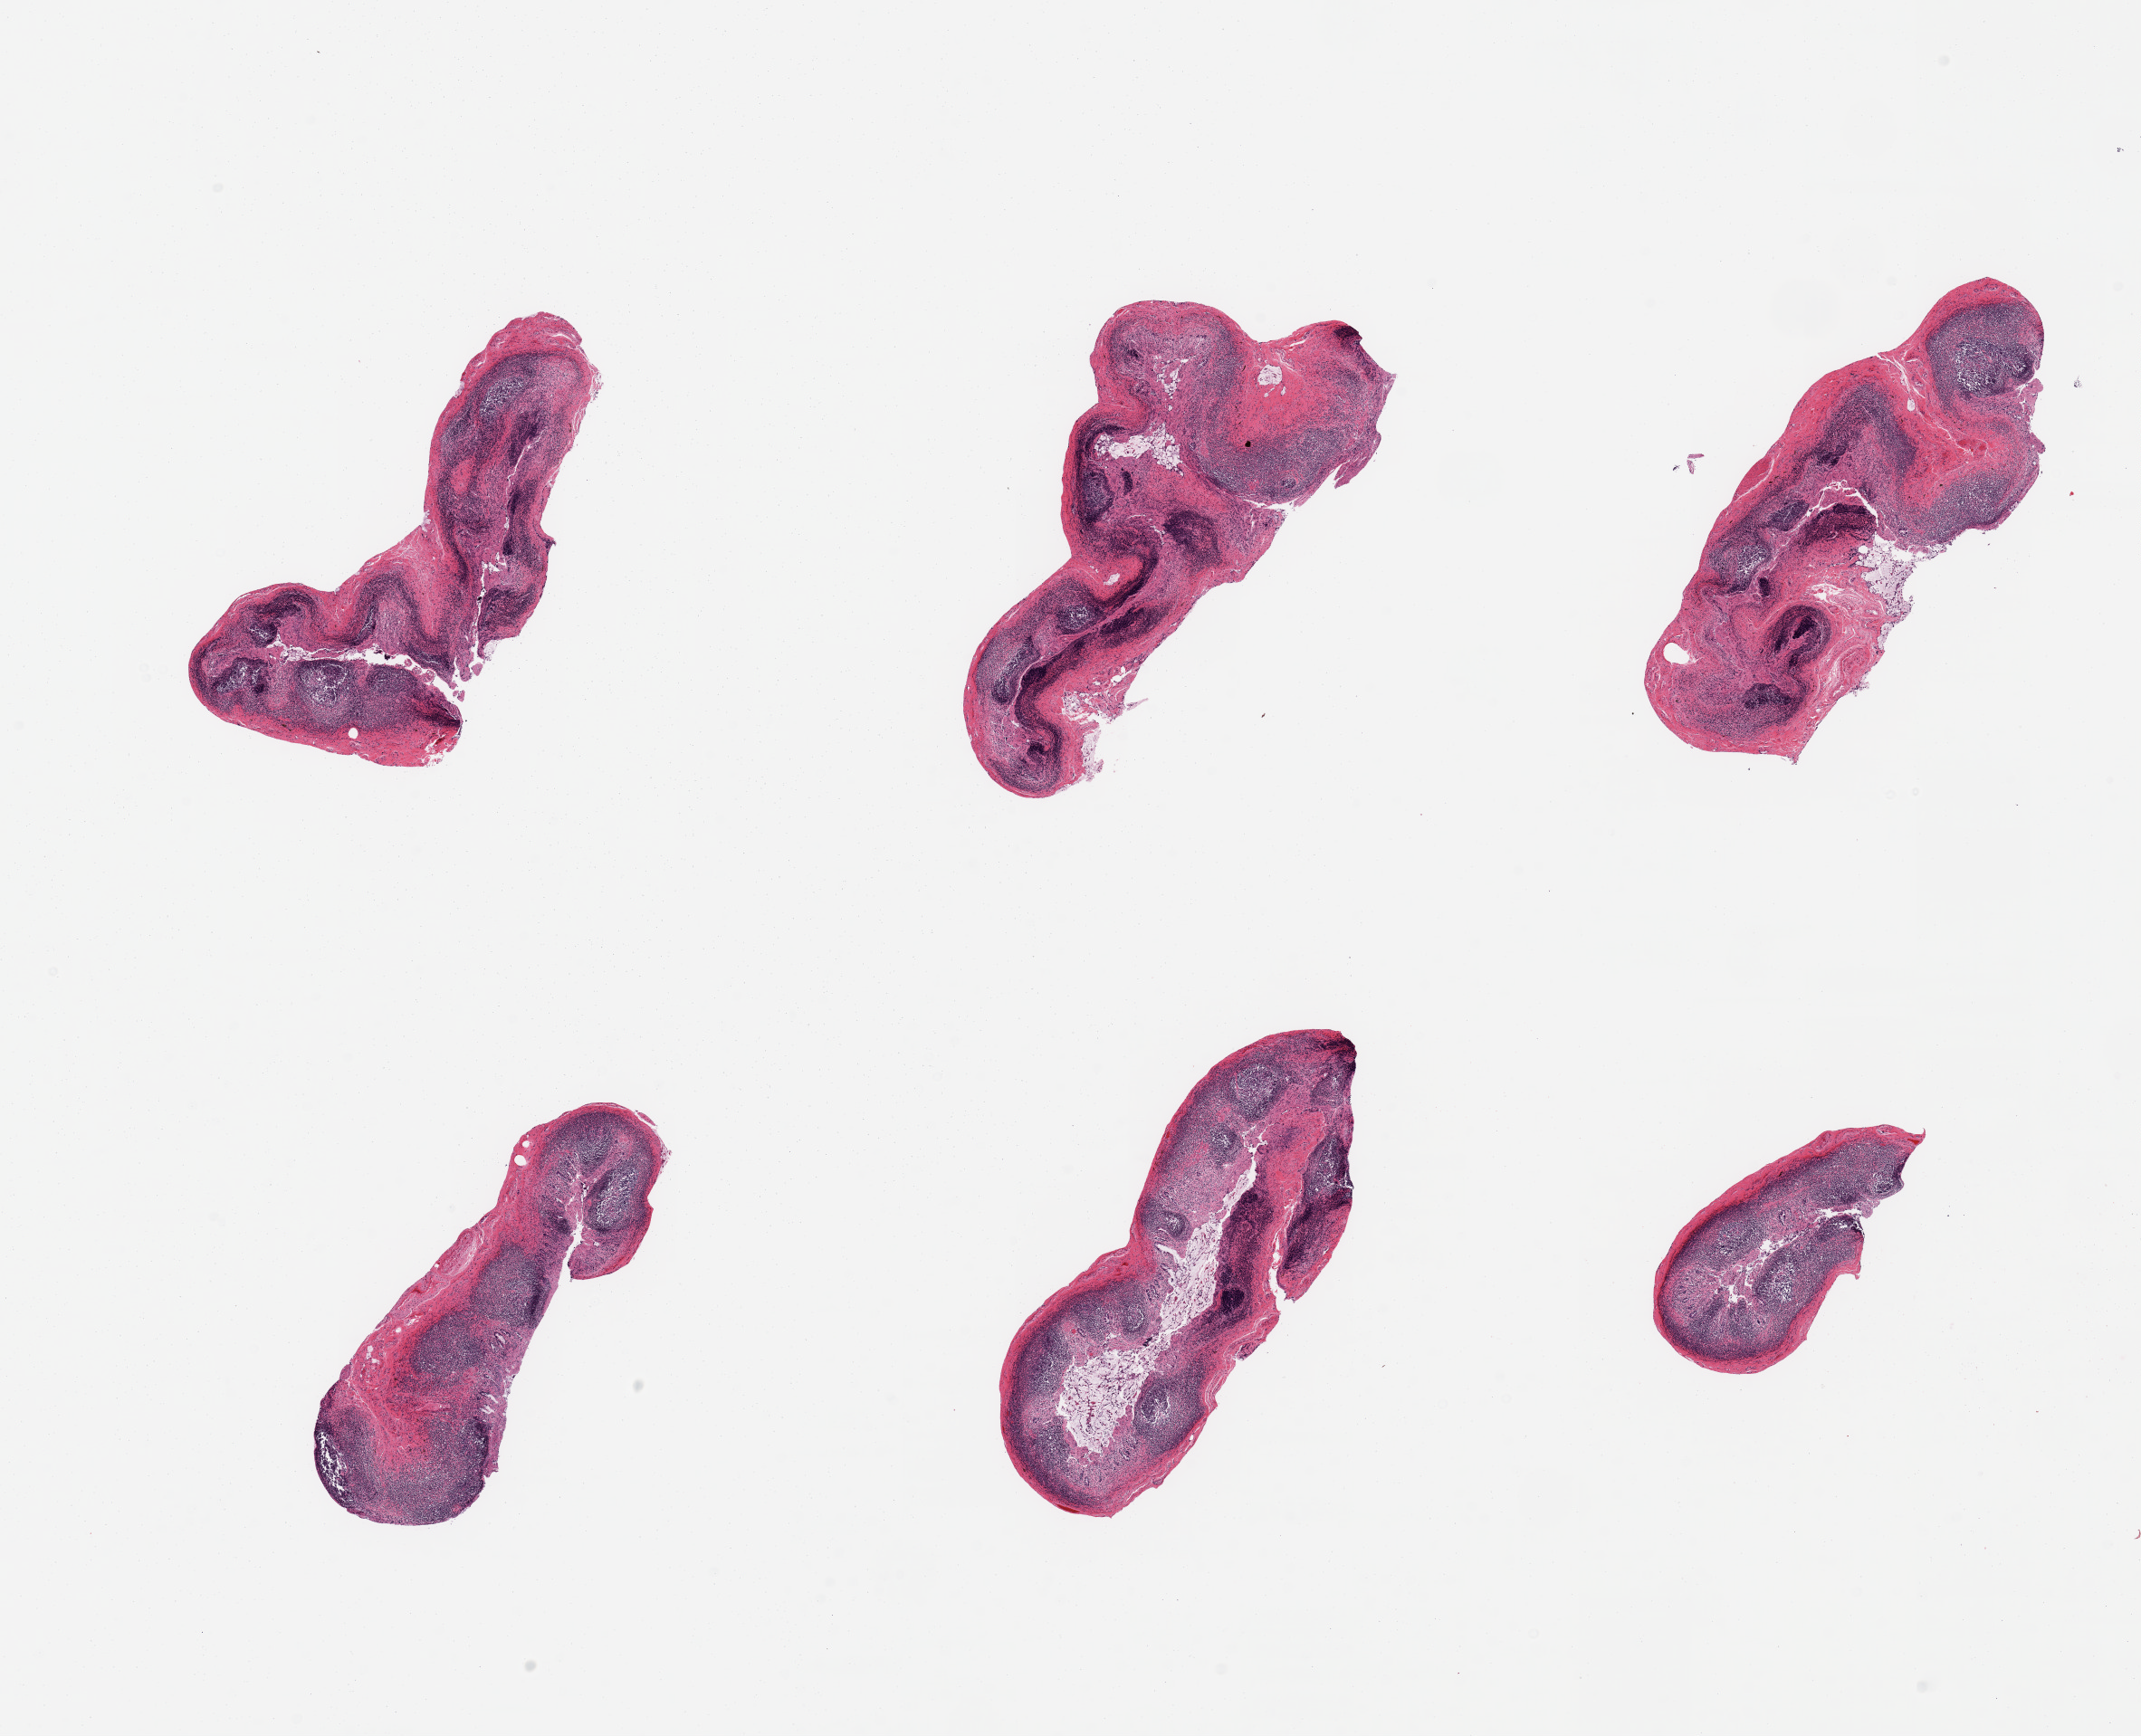
Digitized haematoxylin and eosin-stained section, whole scanned area (about 18.7 x 15.2 mm) shown as a low-resolution overview, PAXgene-fixed paraffin-embedded (PFPE) section, sampled site (target tissue): ileum, tissue donor sample. Donor sex: male.
Reviewer comment on this tissue sample: 6 pieces, target lymphoid aggregates are ~30-40% of tissue.